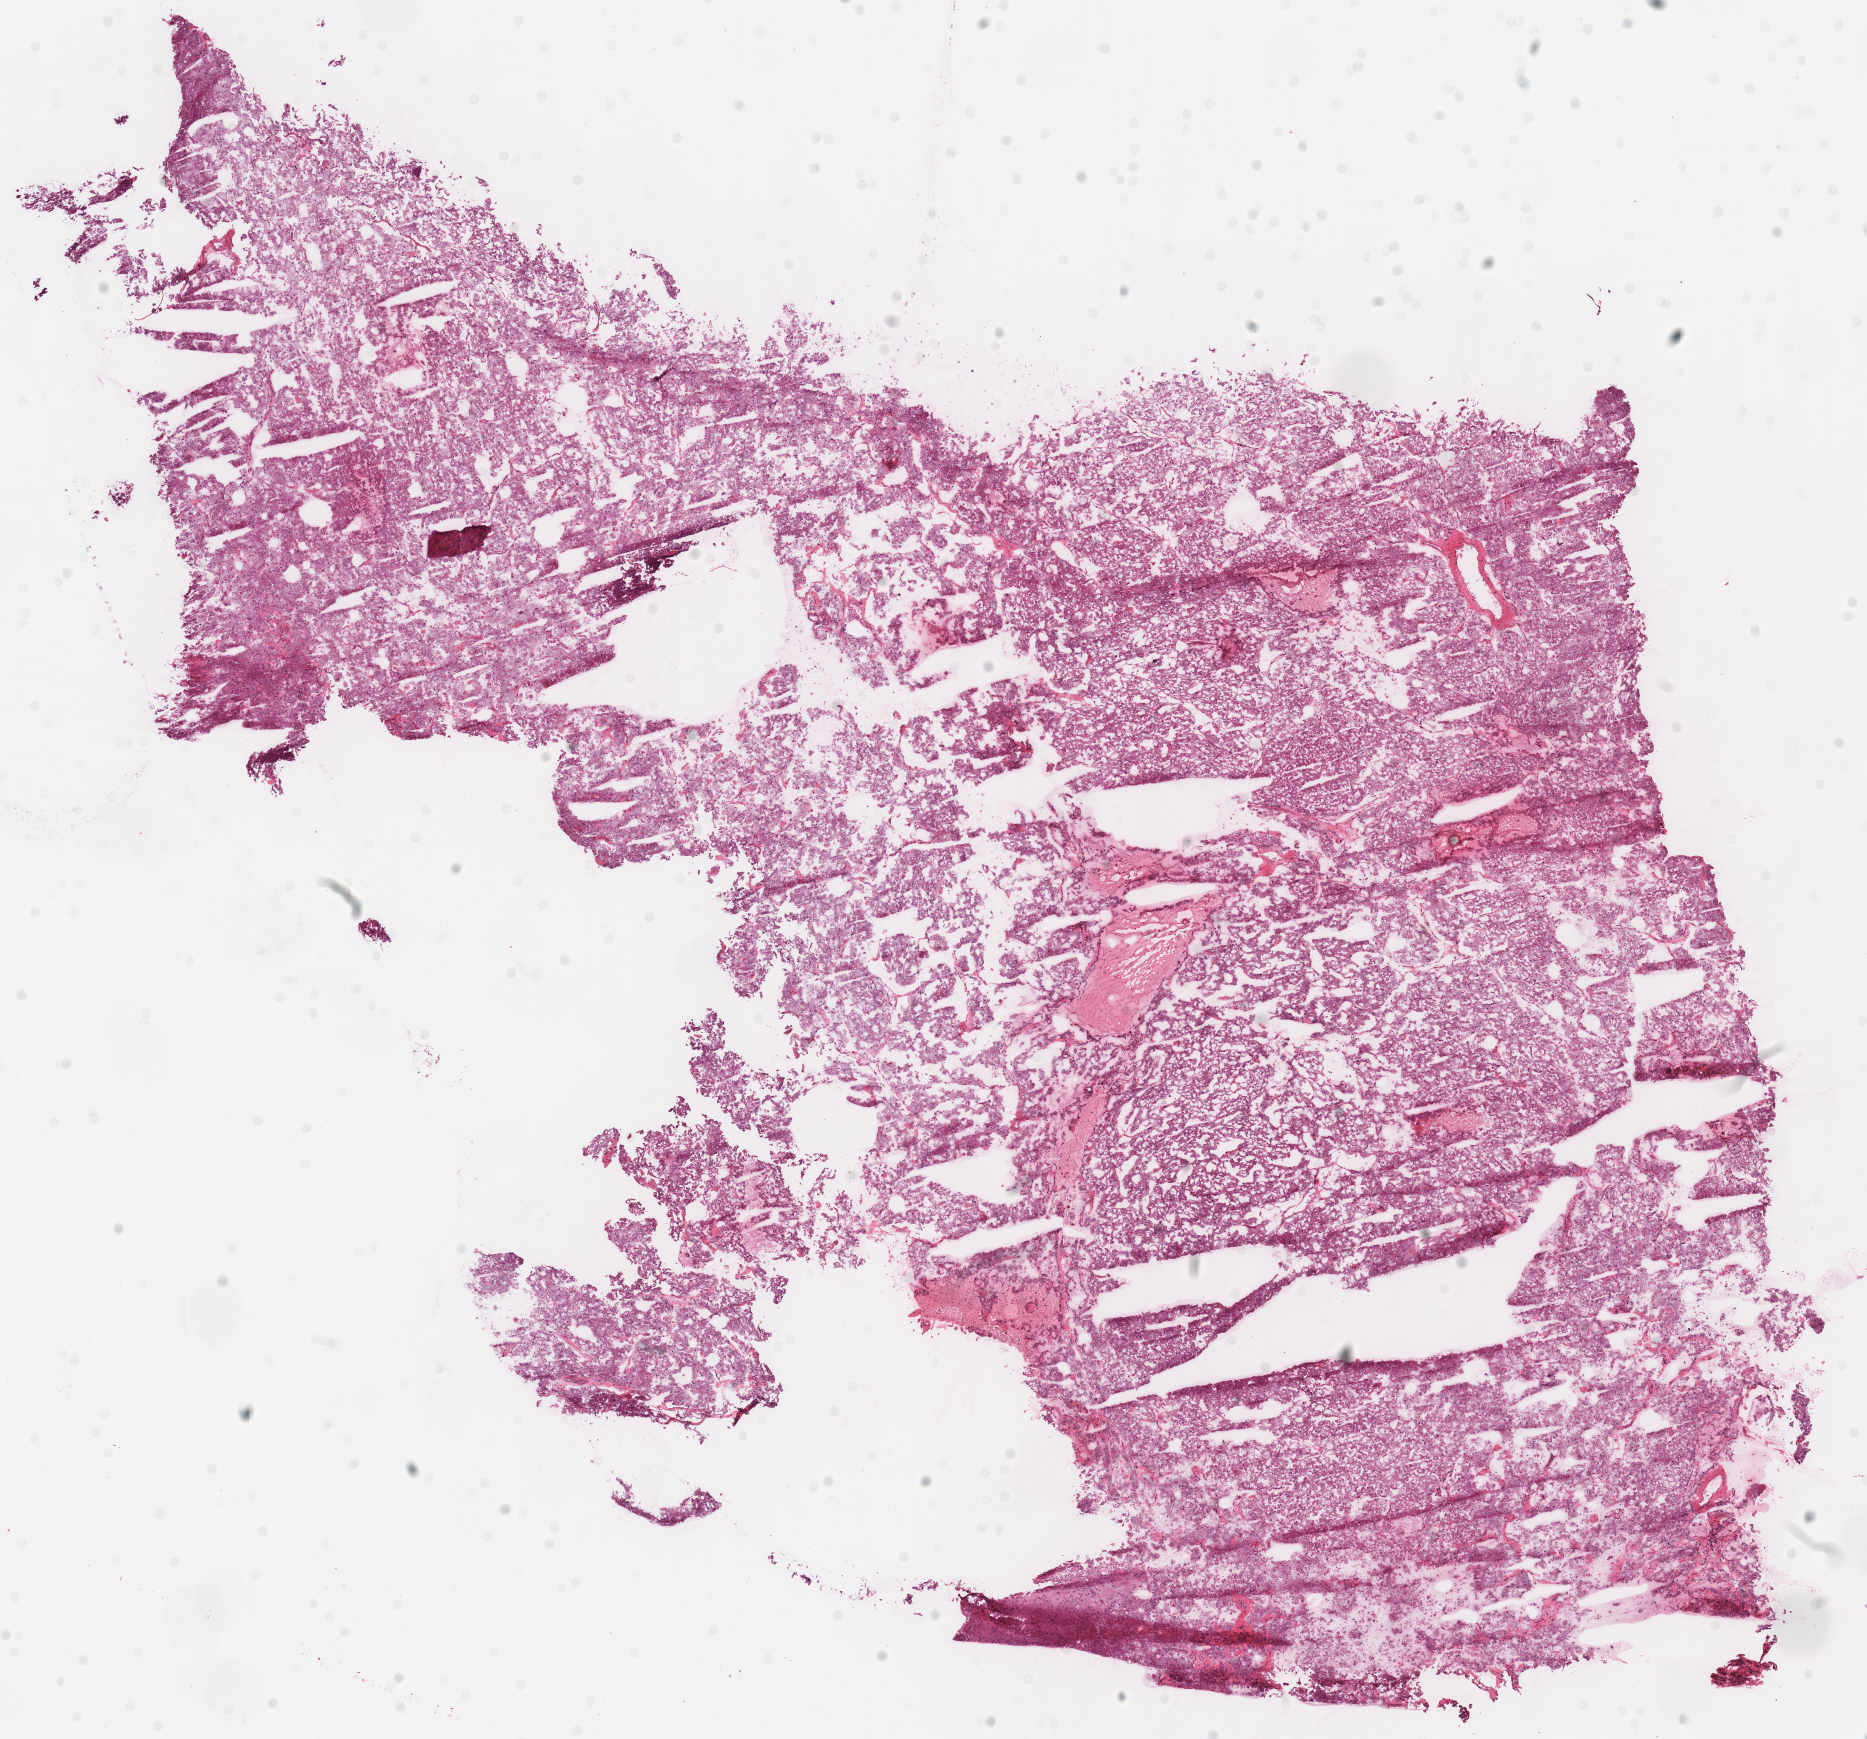
Whole-slide histology image, Hematoxylin and eosin (H&E) stained, shown as a low-resolution overview of the whole scanned area (about 14.7 x 13.7 mm); frozen section from the top of the tissue portion; sample: primary tumour, kidney. Male, age 51 years at initial diagnosis. Slide review estimates, as recorded: tumour cells 95%, tumour nuclei 95%, normal cells 0%, stromal cells 5%, necrosis 0%.
- AJCC pathologic stage: III
- pathologic diagnosis: Renal cell carcinoma, chromophobe type